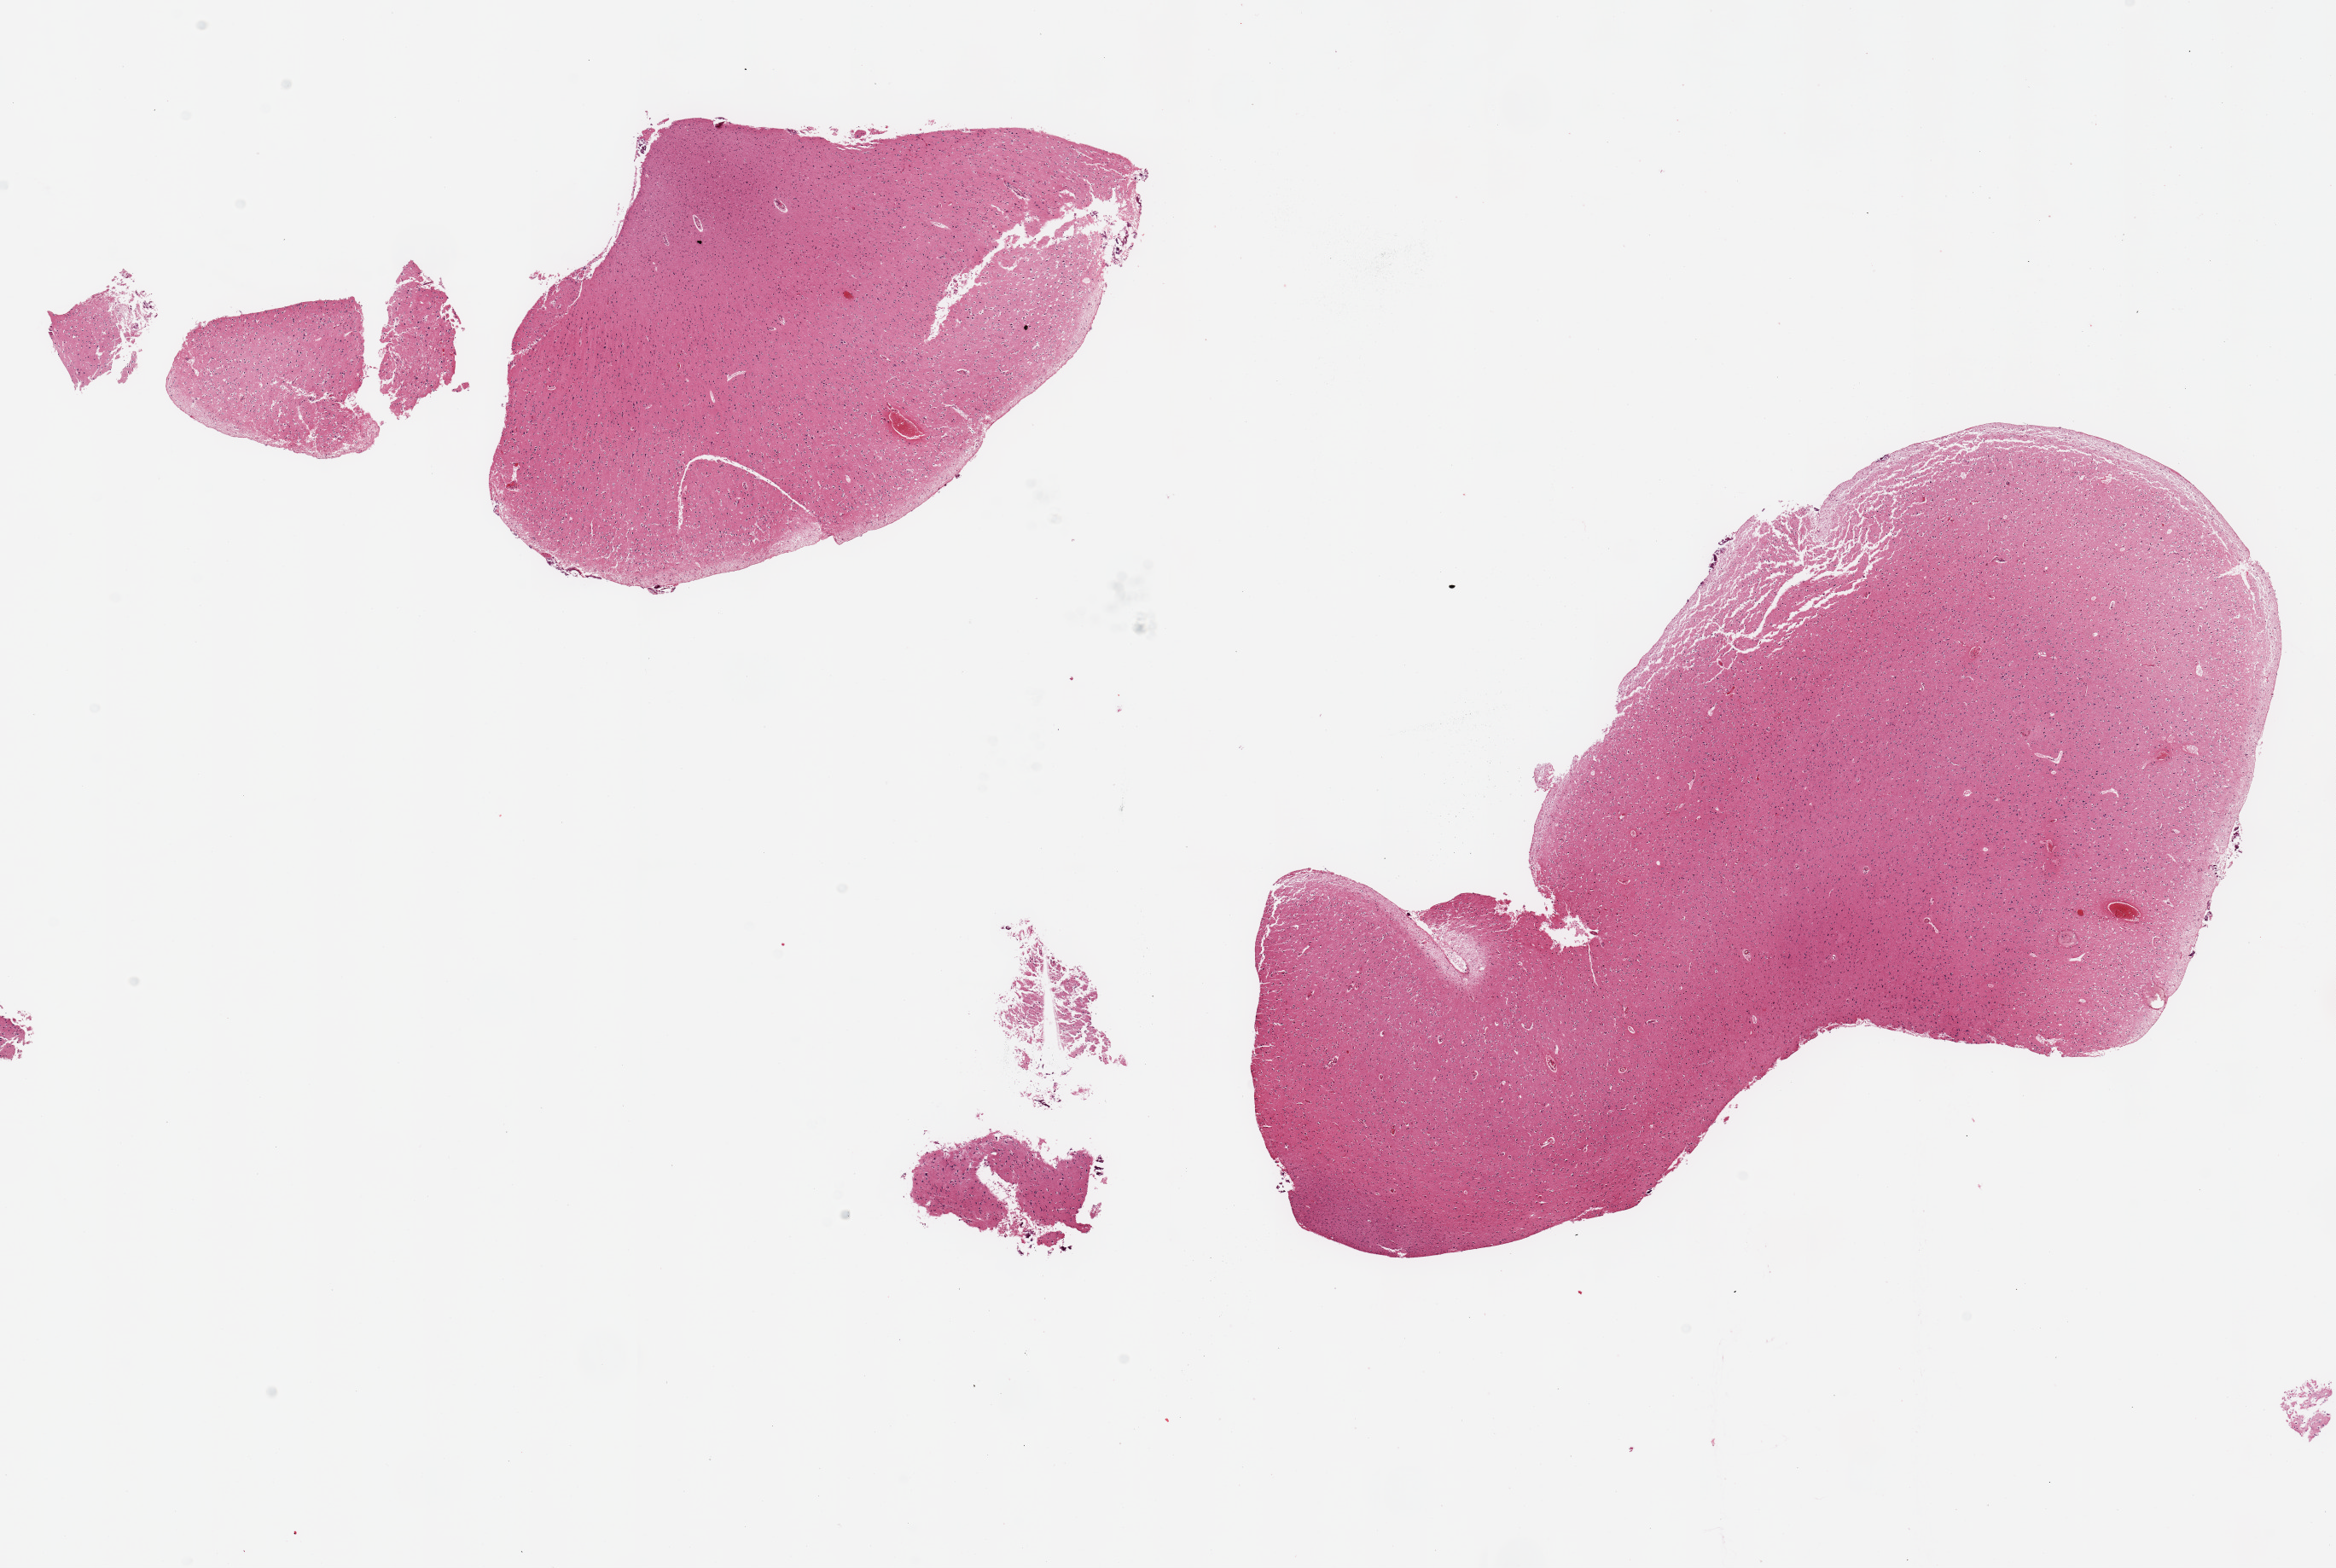
Haematoxylin and eosin whole-slide image — low-resolution overview of the scanned area, about 21.7 x 14.5 mm (from a 20x scan), PAXgene-fixed, paraffin-embedded tissue, section of cerebral cortex (target tissue), tissue donor sample. Donor sex: male.
Reviewer comment on this tissue sample: 2 pieces and few fragments; cerebral cortex, not cerebellum.